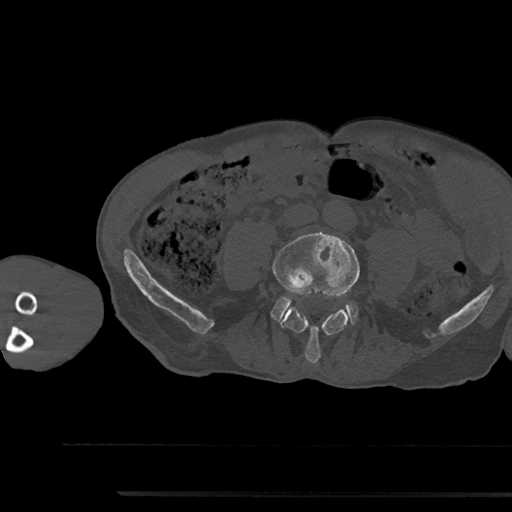
CT including the spine, one axial slice; slice 391 of 797 in the series (ordered by position); 120 kVp; bone window (W 1800 / L 400 HU); 0.5 mm slice thickness; 512 × 512 image matrix, field of view 367 × 367 mm. Male patient, age 79 years. From the clinical record (not read from this slice): primary cancer: prostate.
Outlined on this slice (semi-automatic segmentation, software-assisted and operator-edited):
- L4 vertebra: box from (x=273, y=231) to (x=359, y=363) px
- L5 vertebra: (x=271, y=296)–(x=358, y=324)